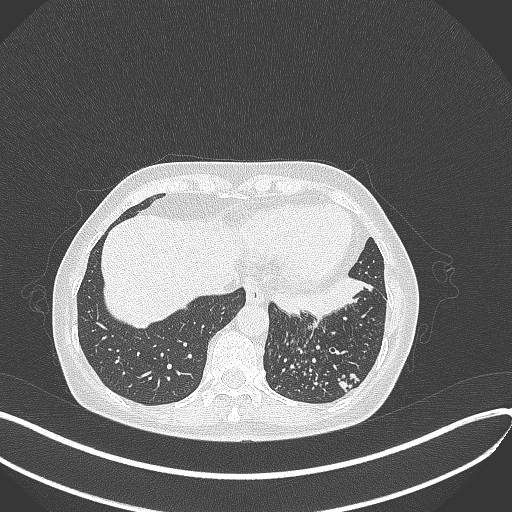
Chest CT, one axial slice; slice 99 of 429 in the series (ordered by position); 100 kVp; lung window (W 1500 / L -600 HU); 512 × 512 image matrix. Patient: female, 63 years. Case-level facts recorded for this patient, not image findings: clinical TNM (as recorded): T1b N0 M0; histopathological grade: G2-3.
Annotated regions visible in this slice (rectangle marked by the reading radiologist):
- lung tumour (recorded histology: adenocarcinoma): box from (x=266, y=272) to (x=376, y=320) px